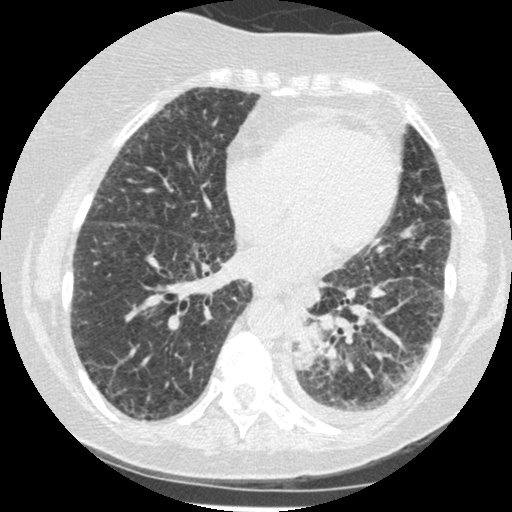
Low-dose screening chest CT, one axial slice; position 81 of 341 along the scan axis; lung window (W 1500 / L -600 HU); 1.25 mm slice thickness; 512 × 512 image matrix, field of view 310 × 310 mm.
Structures marked on this image (expert manual segmentation):
- lesion 1 (tumor, lower lobe of left lung): bounding box (x1, y1, x2, y2) in pixels: (292, 322, 322, 369)